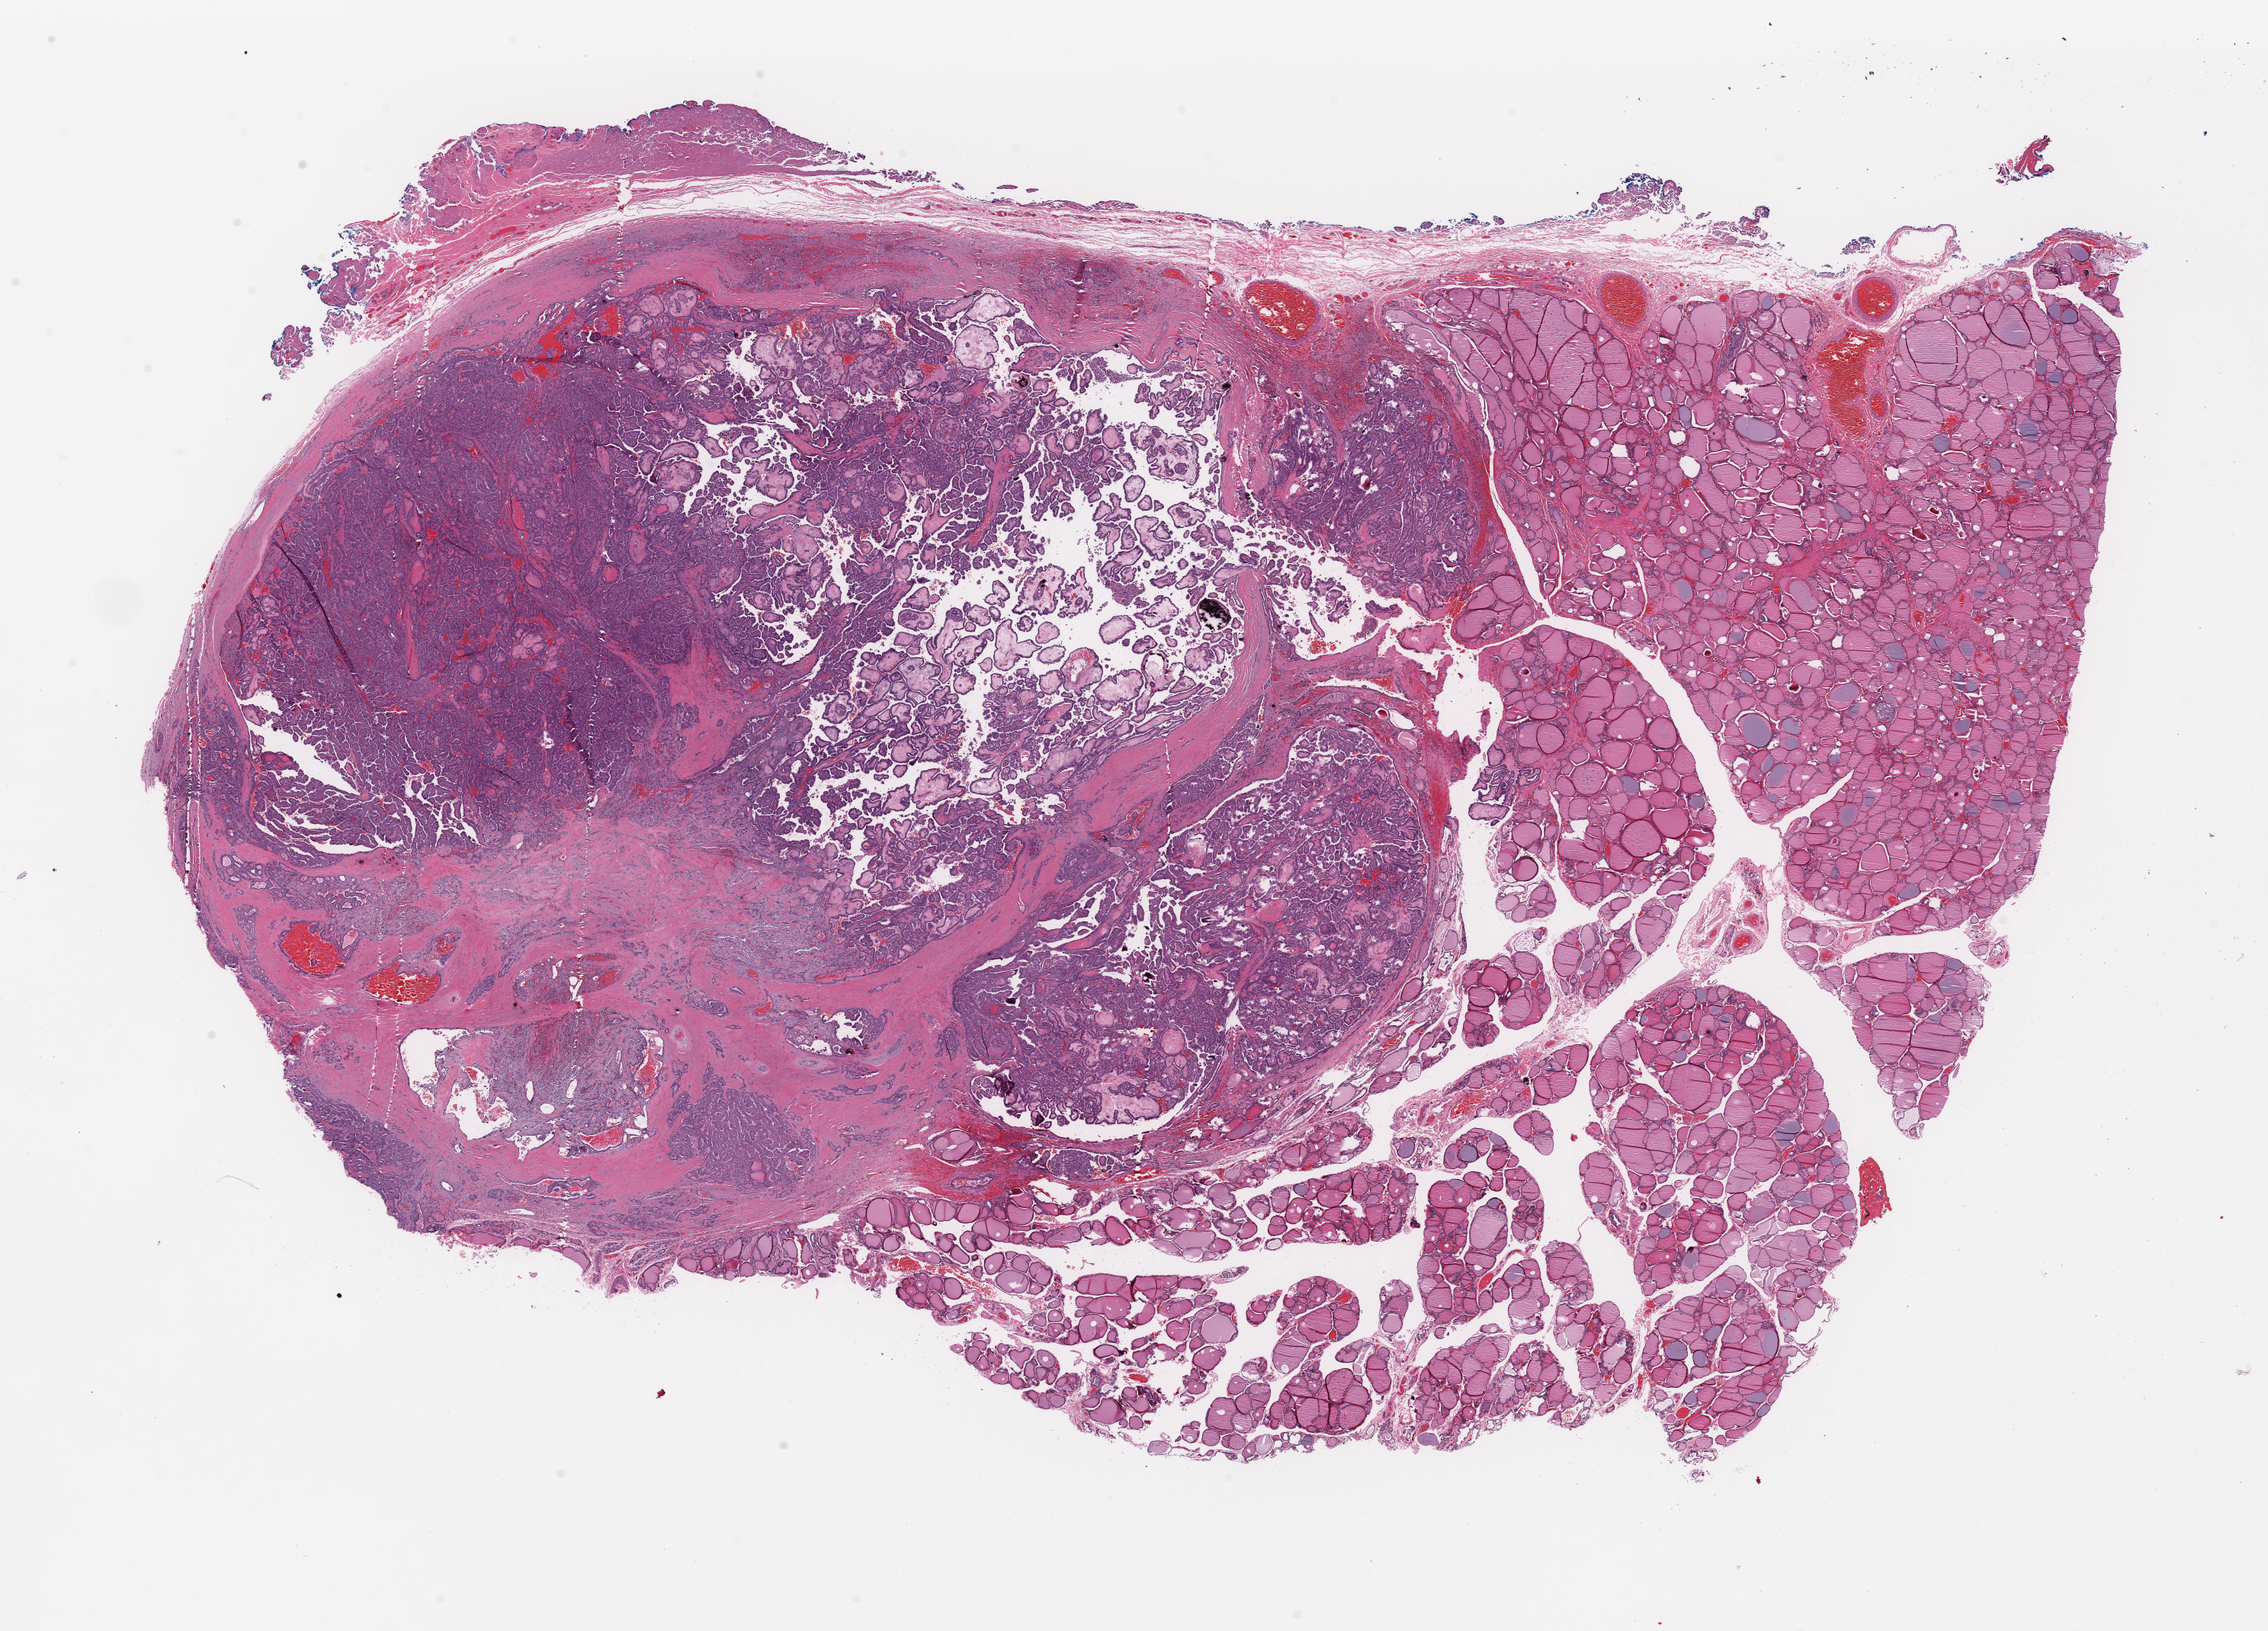
Hematoxylin and eosin (H&E) stained whole-slide image, shown as a low-resolution overview of the whole scanned area (about 23.5 x 16.9 mm, from a 40x scan). FFPE section. Thyroid, primary tumour sample. Female, age 28 years at initial diagnosis.
AJCC pathologic stage: I (7th edition). TNM: T3 N1b M0. Lymph nodes positive (case pathology): 8 of 16 examined. Diagnosis: Papillary carcinoma, columnar cell (thyroid gland).